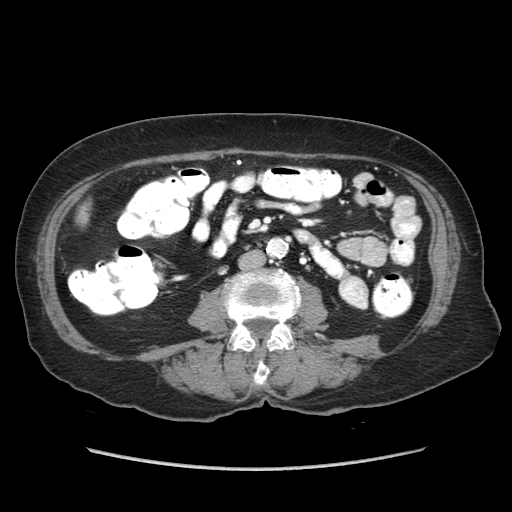
Contrast-enhanced abdominal CT (liver protocol), one axial slice. Reconstruction kernel STANDARD. Soft-tissue window (W 400 / L 40 HU). 2.5 mm slice thickness. 512 × 512 image matrix. From the clinical record (not read from this slice): diagnosis: hepatocellular carcinoma (patient treated with transarterial chemoembolisation; whether this scan precedes or follows treatment is not stated here); TNM stage (as recorded): Stage-IIIA; Child-Pugh class: A.
Structures marked on this image (semi-automatically segmented with operator editing):
- liver parenchyma outside the tumour (the mass and vessels are separate outlines, so this box may not span the whole liver): bounding box (x1, y1, x2, y2) in pixels: (78, 206, 88, 222)